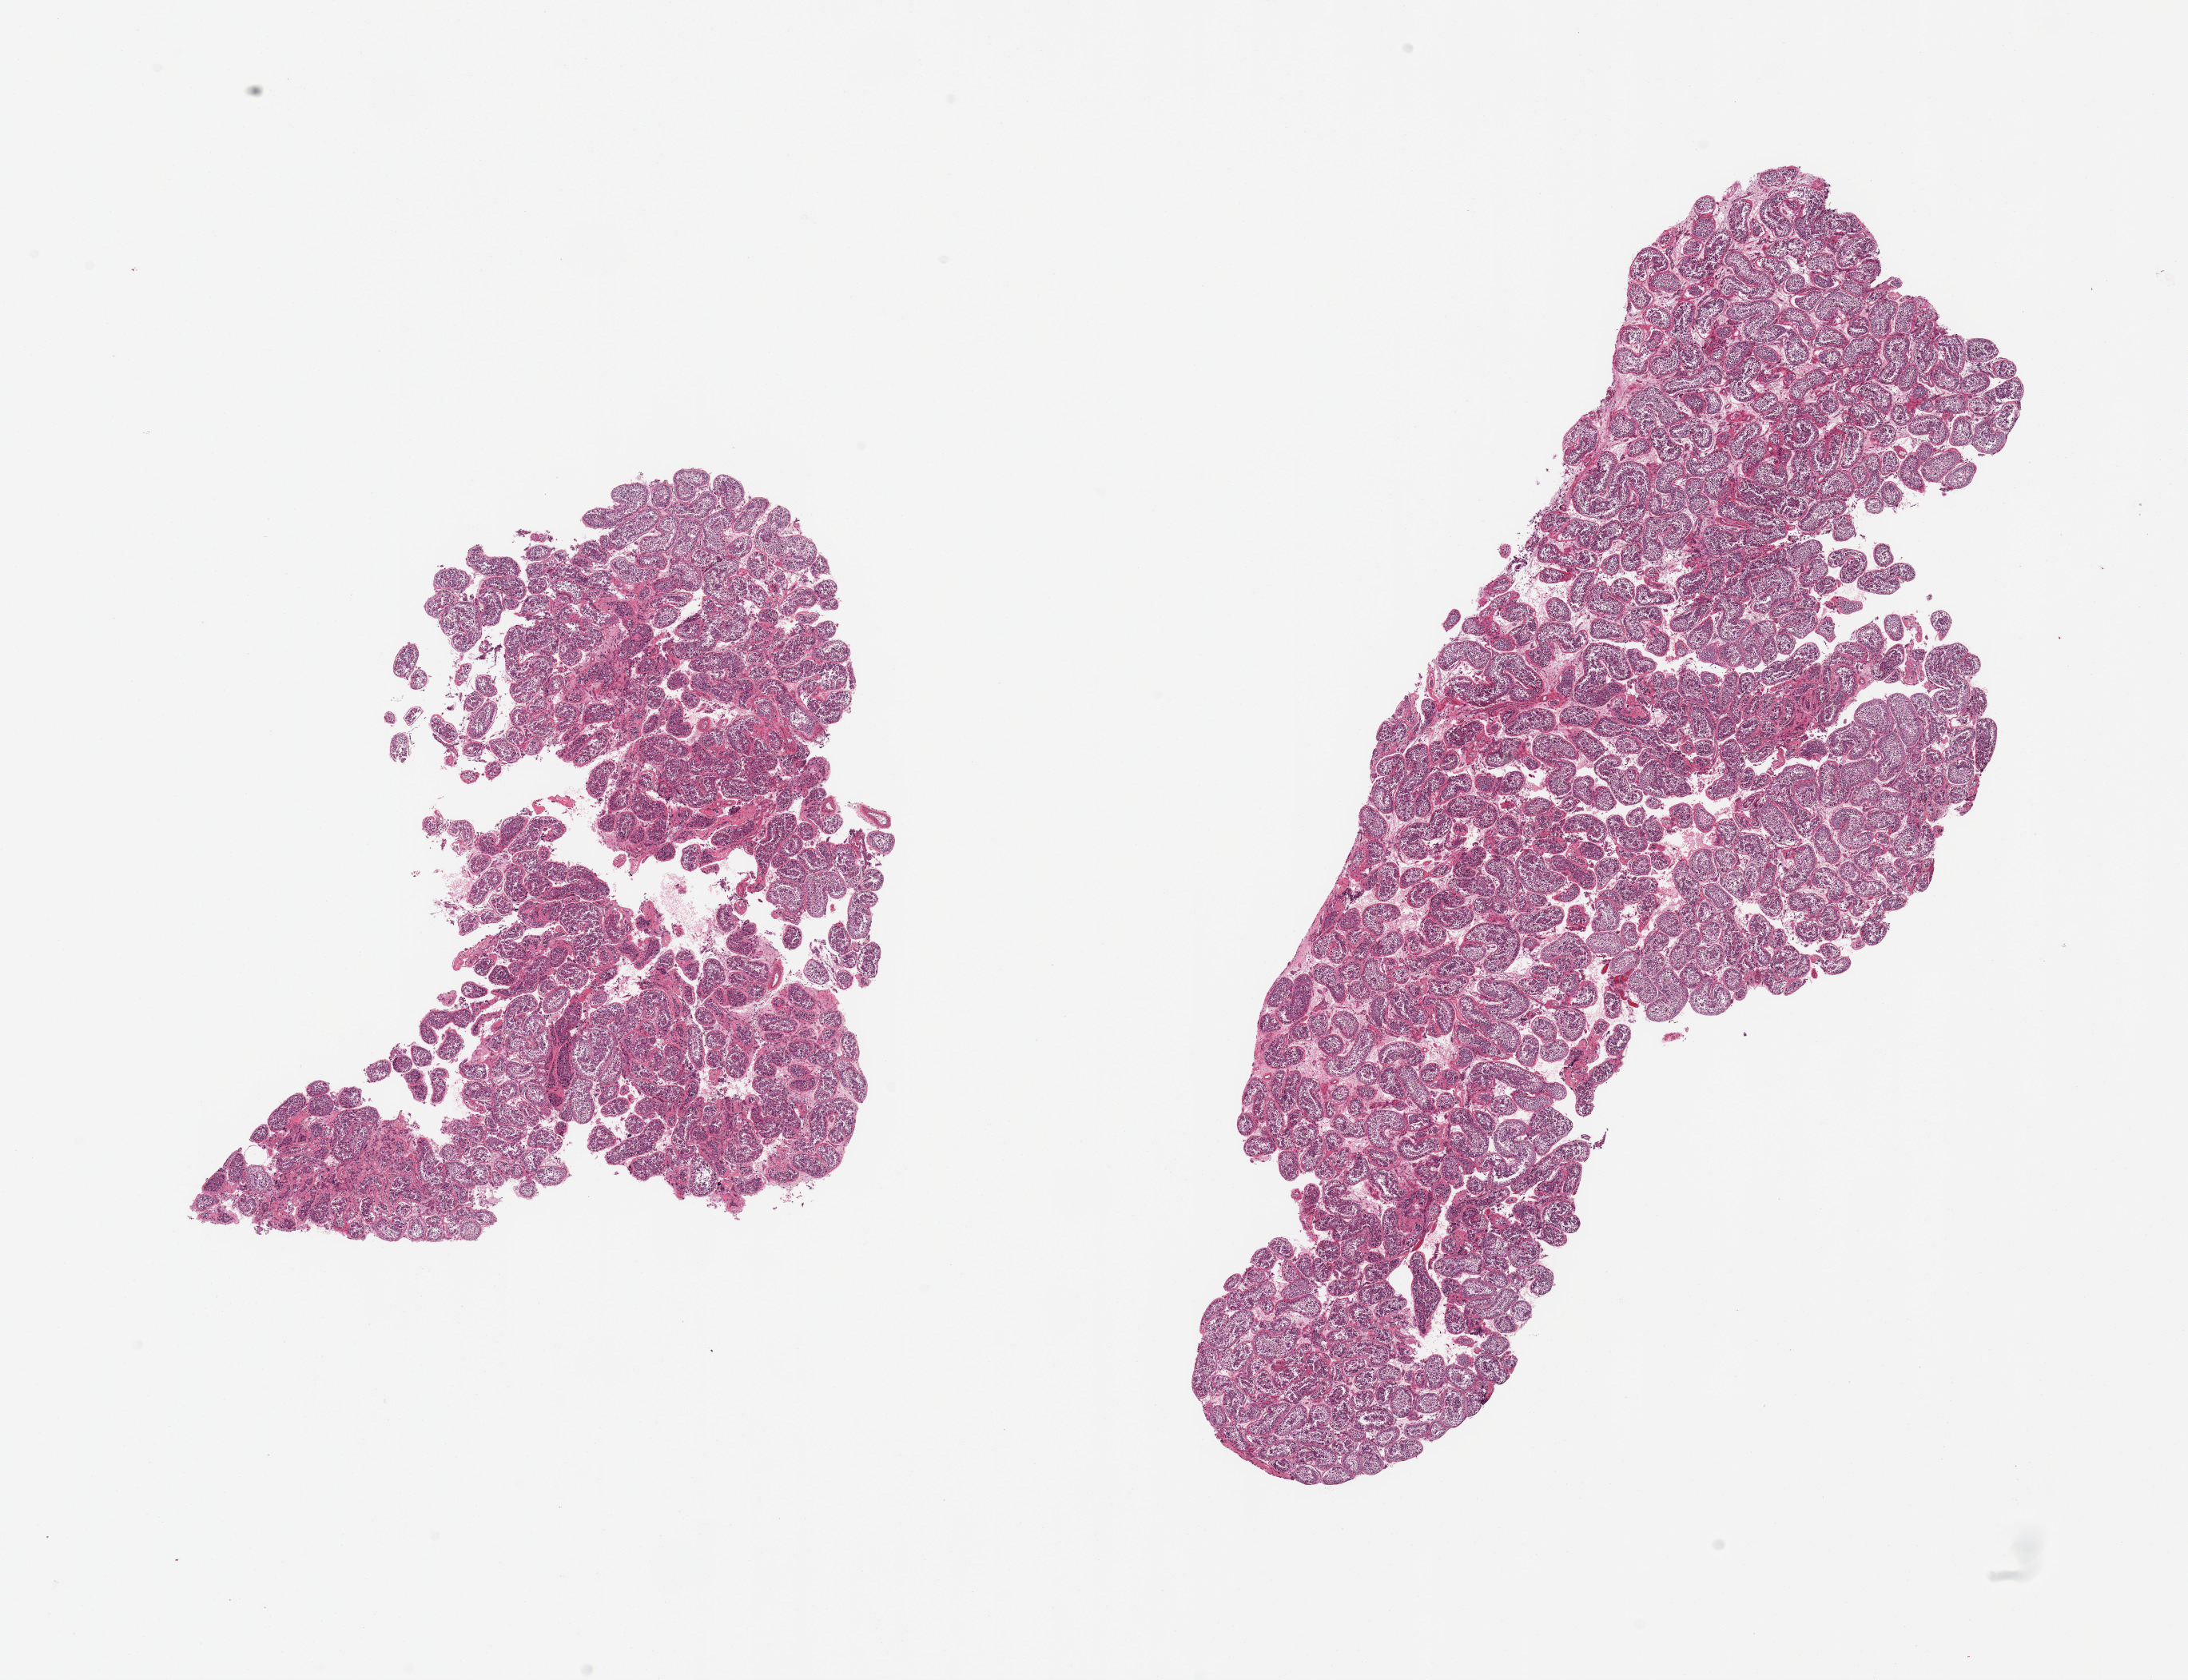
Haematoxylin and eosin whole-slide image, a low-resolution overview of the entire scanned area, about 21.7 x 16.6 mm (acquisition: 20x scan); PAXgene-fixed paraffin-embedded (PFPE) section; sampled site (target tissue): testis; tissue donor sample. Donor sex: male.
Review note (as recorded): 2 pieces; active spermatogenesis.